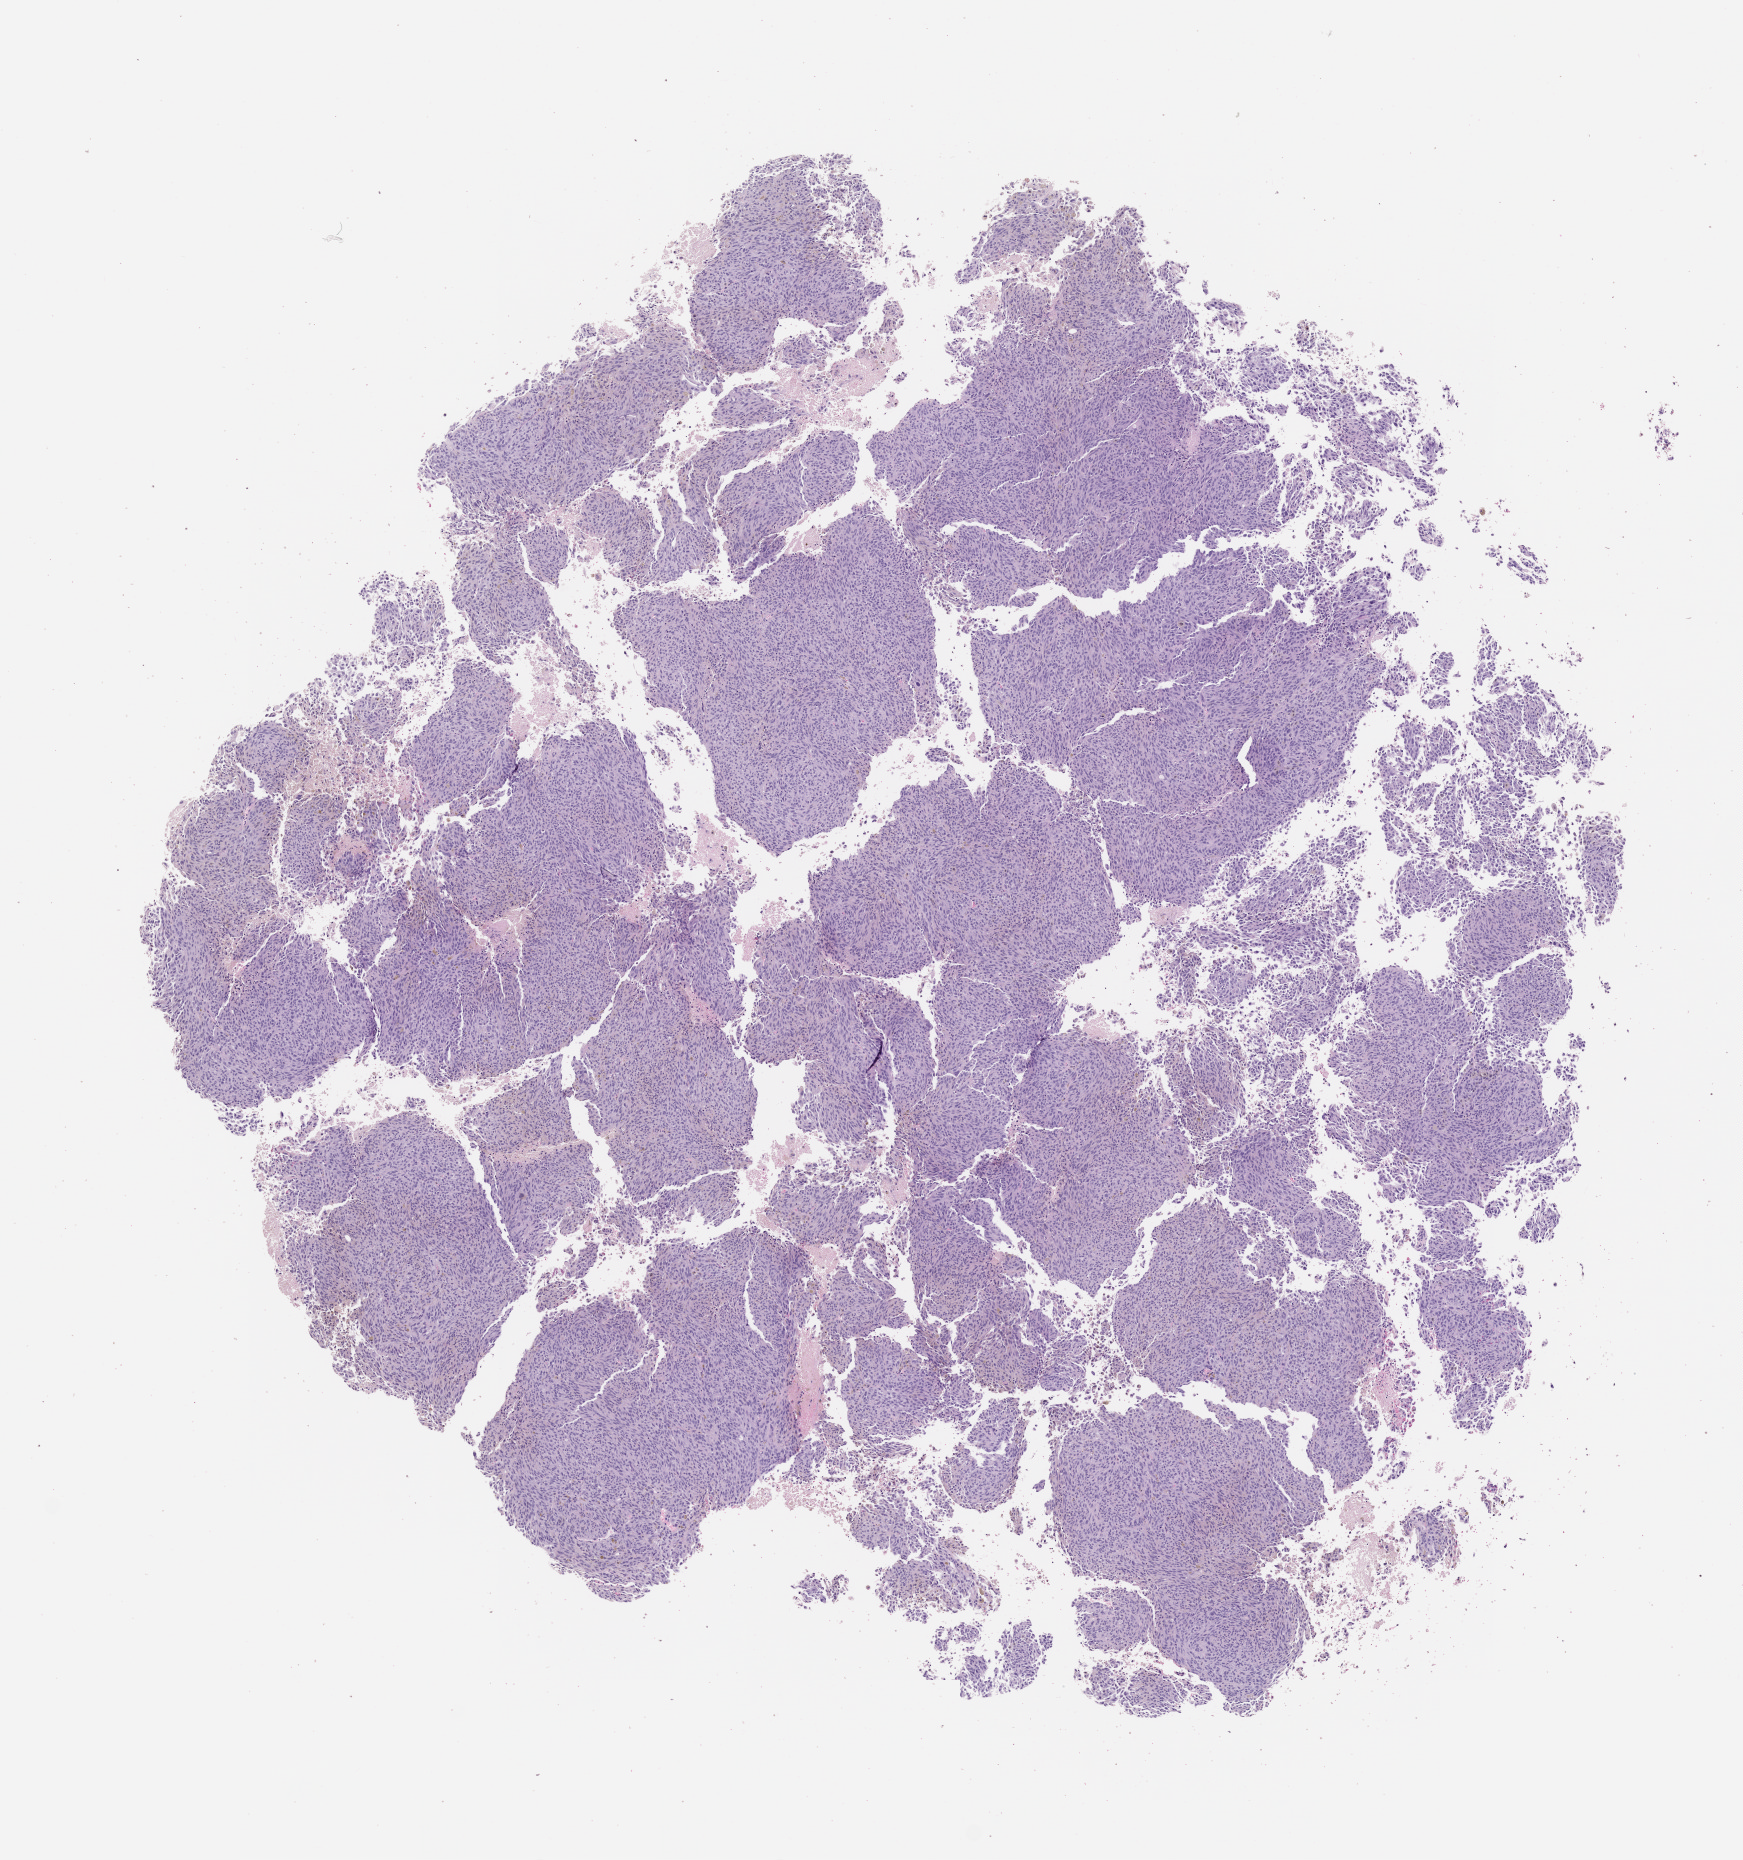
Whole-slide image, hematoxylin and eosin (H&E): patient-derived xenograft (human tumor grown in a mouse), passage 0, a low-resolution overview of the entire scanned area, about 7.0 x 7.5 mm. FFPE section. Tumor site category: skin.
• originating patient diagnosis: Melanoma